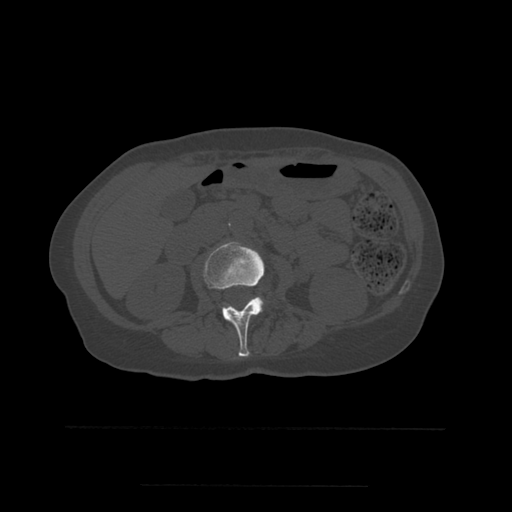
CT including the spine, one axial slice. Slice 206 of 544 in the series (ordered by position). Bone window (W 1800 / L 400 HU). 512 × 512 image matrix, field of view 350 × 350 mm. Patient age 58 years. From the clinical record (not read from this slice): primary cancer: lung.
Structures marked on this image (semi-automatically segmented with operator editing):
- L2 vertebra: bounding box [x1, y1, x2, y2] px = [204, 242, 265, 357]